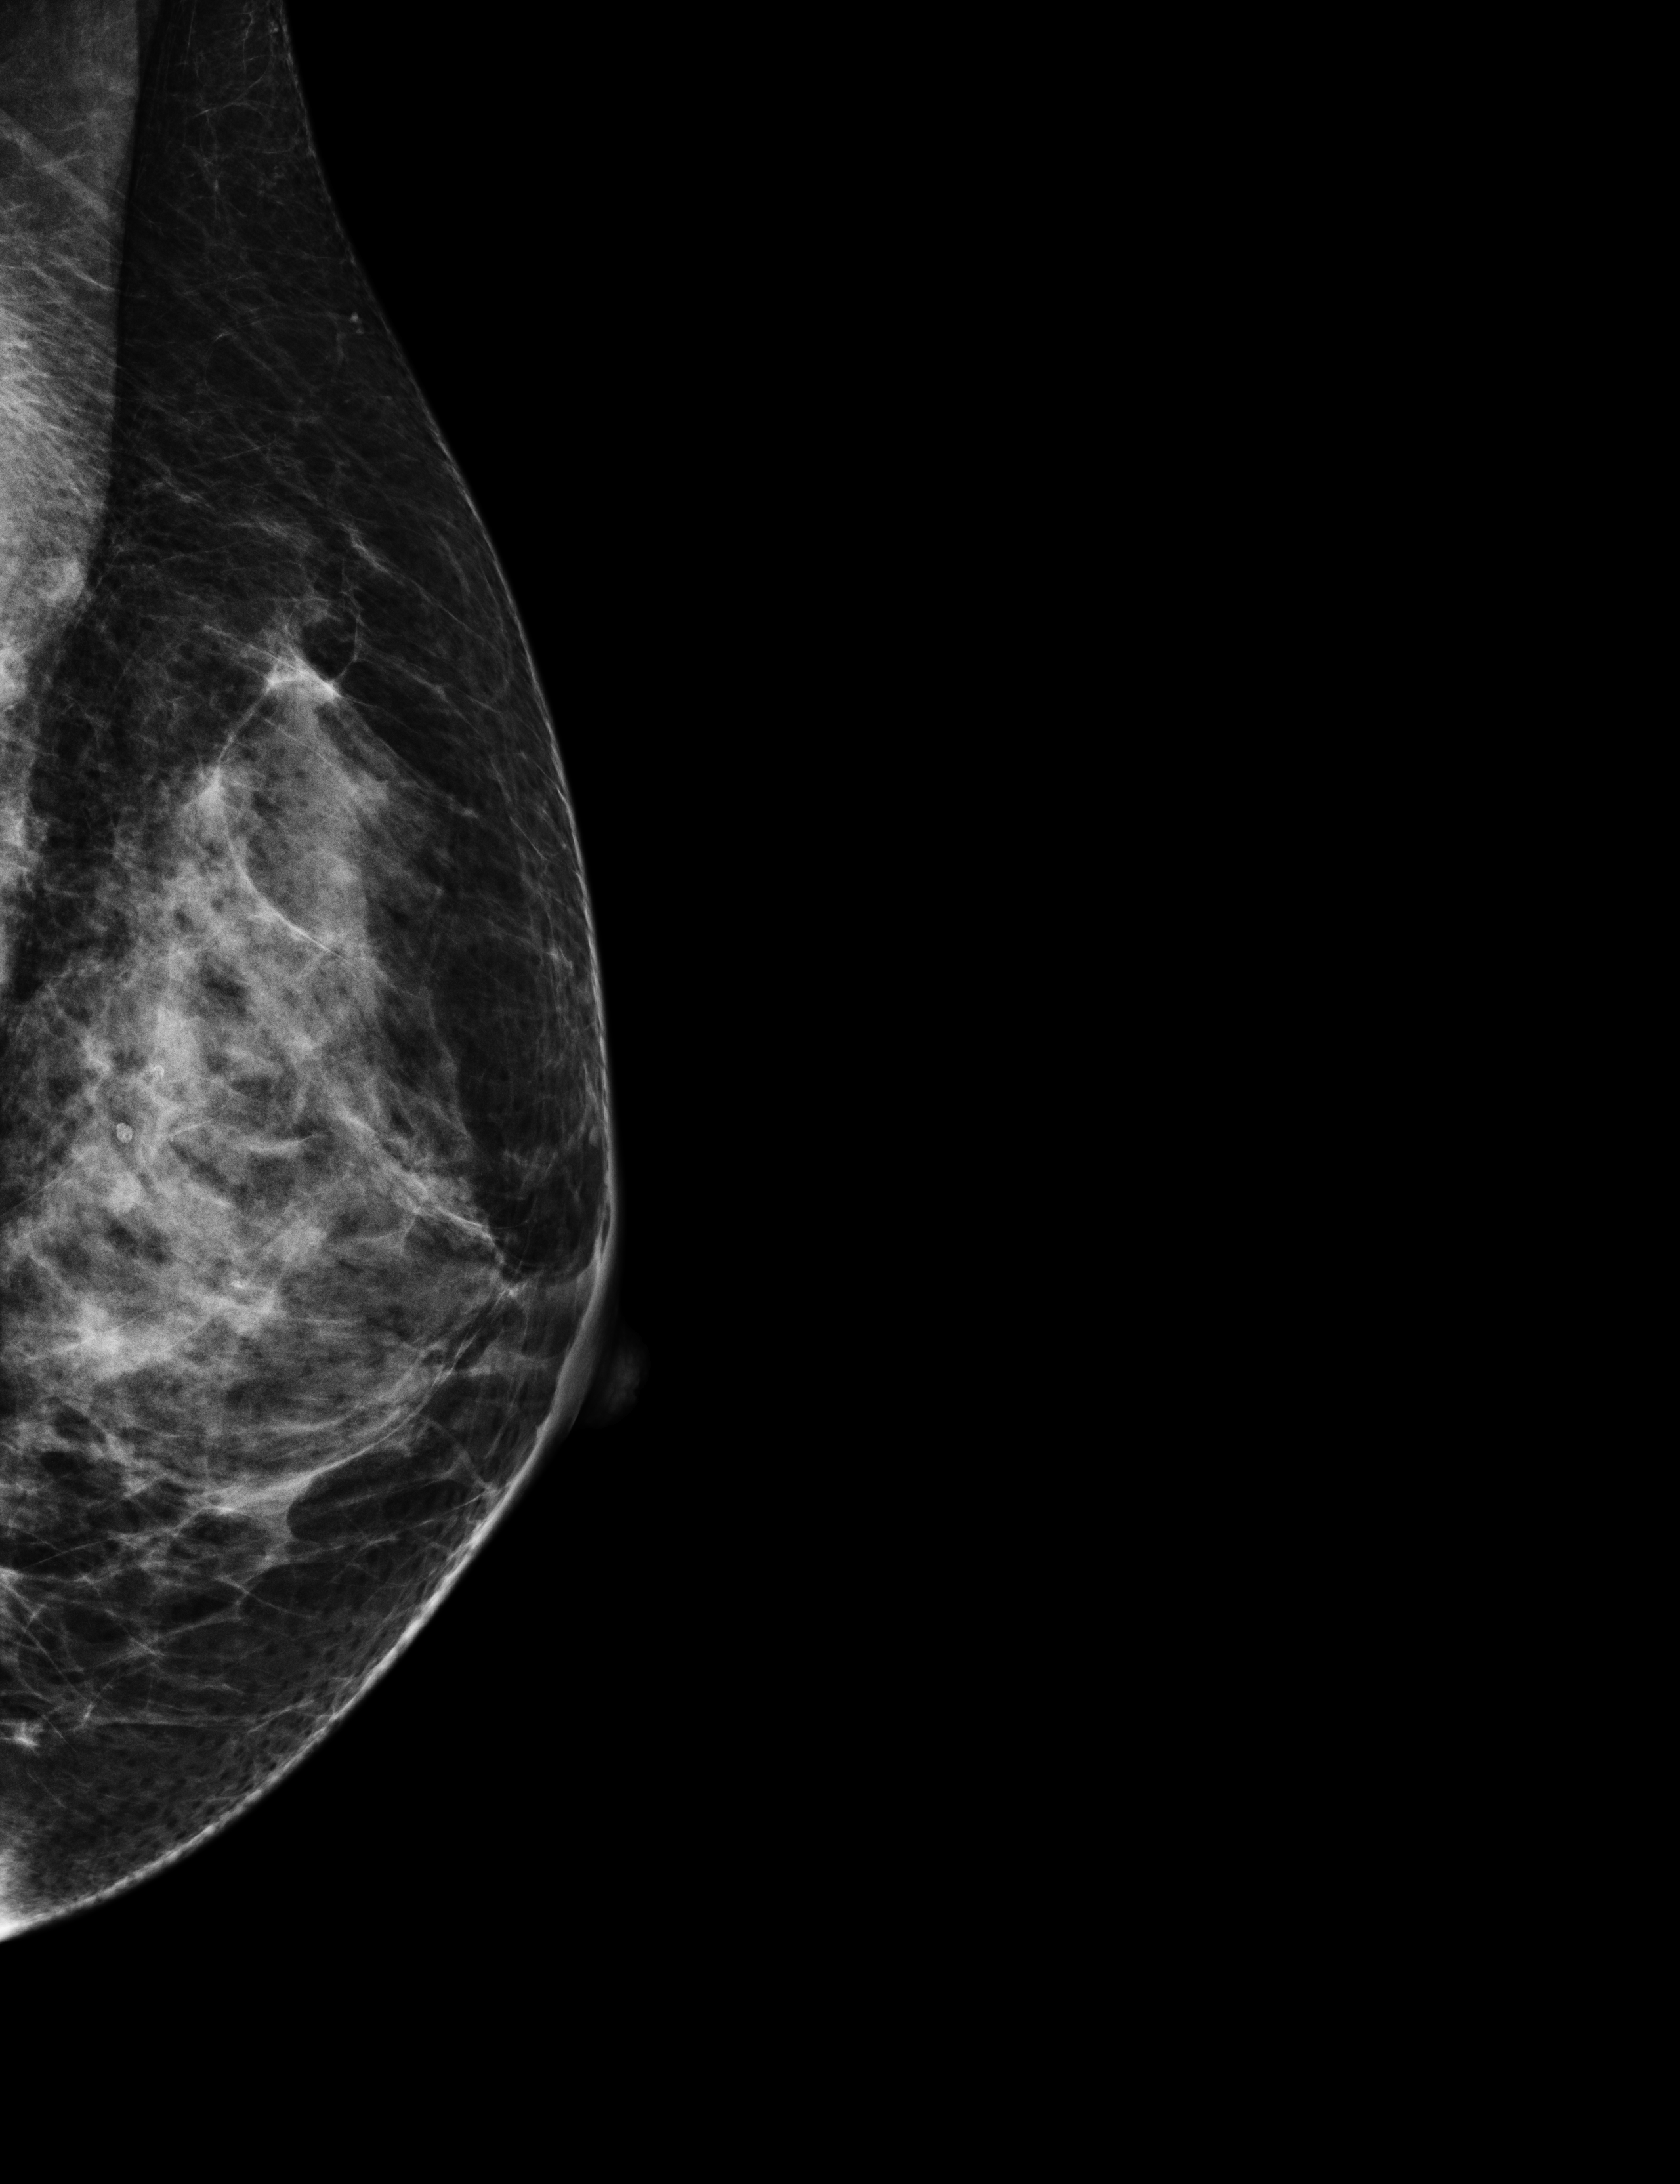
Annual screening mammography examination, system: Selenia Dimensions. Female patient, age 44 years.
Image type: full-field digital mammogram. Breast: left. Projection: exaggerated CC view (lateral).